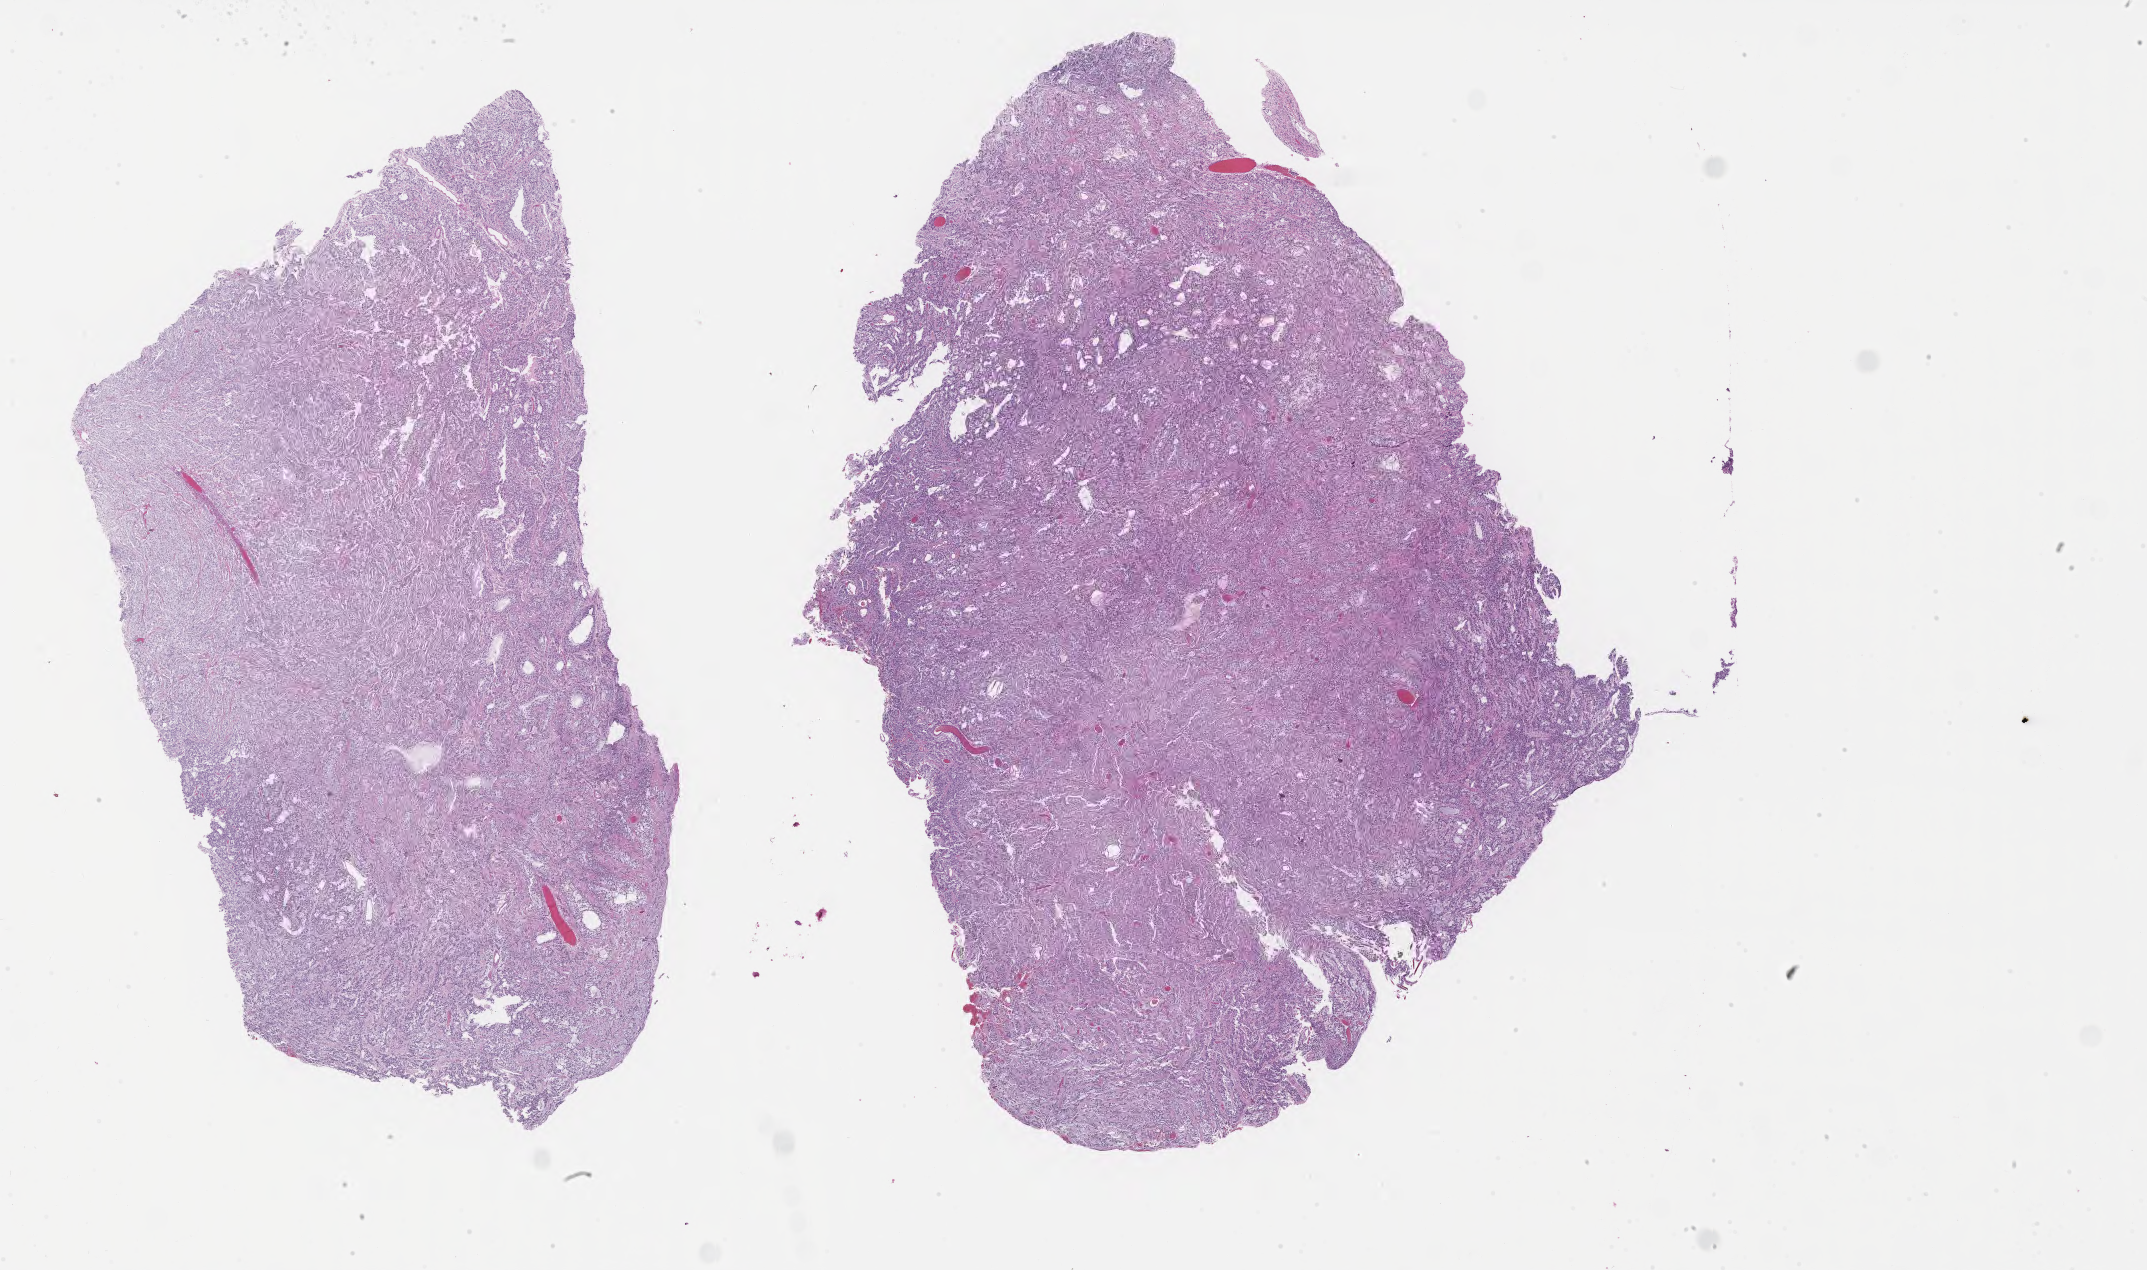
Digitized haematoxylin and eosin-stained section of tumor tissue from the parietal lobe, whole scanned area (about 34.7 x 20.5 mm) shown as a low-resolution overview, formalin-fixed paraffin-embedded section. Patient female; age 131 months (10 years 11 months).
• recorded diagnosis: Glioma, malignant